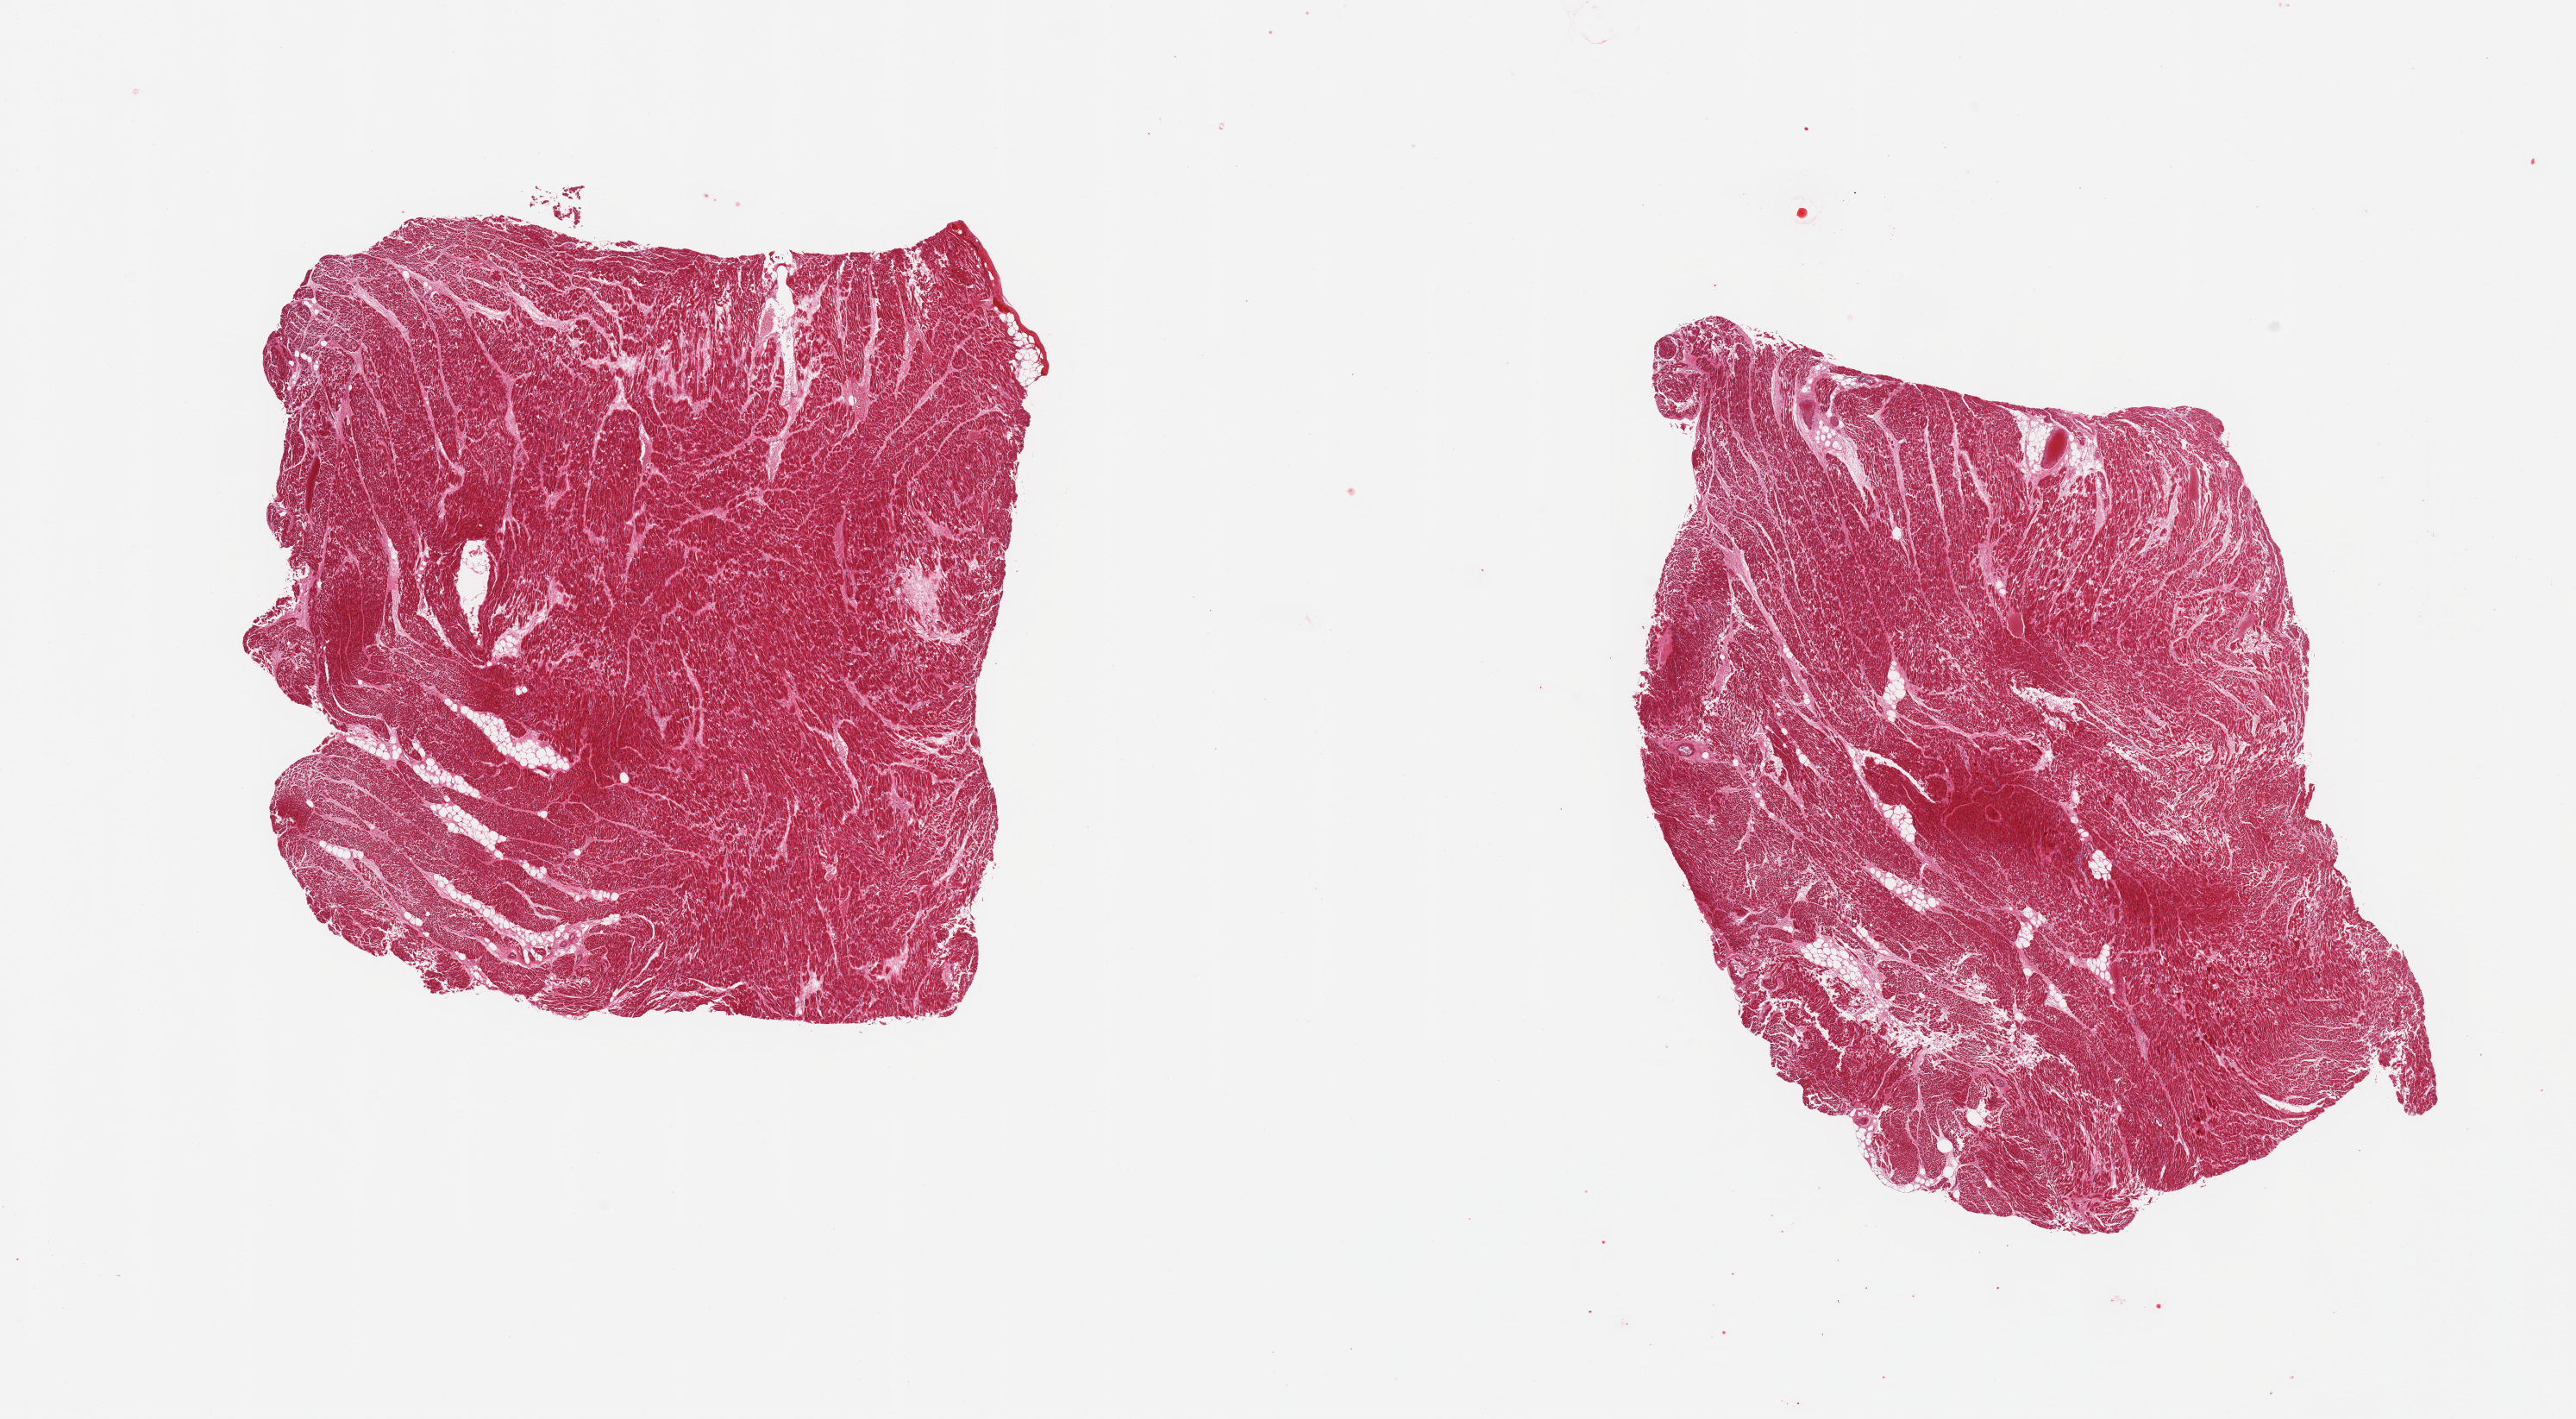
Digitized H&E-stained section, a low-resolution overview of the entire scanned area, about 23.6 x 13.0 mm (slide scanned at 20x), PAXgene-fixed paraffin-embedded (PFPE) section, section of heart (target tissue), tissue donor sample. Male donor.
Reviewer comment on this tissue sample: 2 pieces; fat infiltration/degeneration ~15%; patchy swelling and eosinophilia of fibers consistent with early stage of myocardial infarction; congestion.